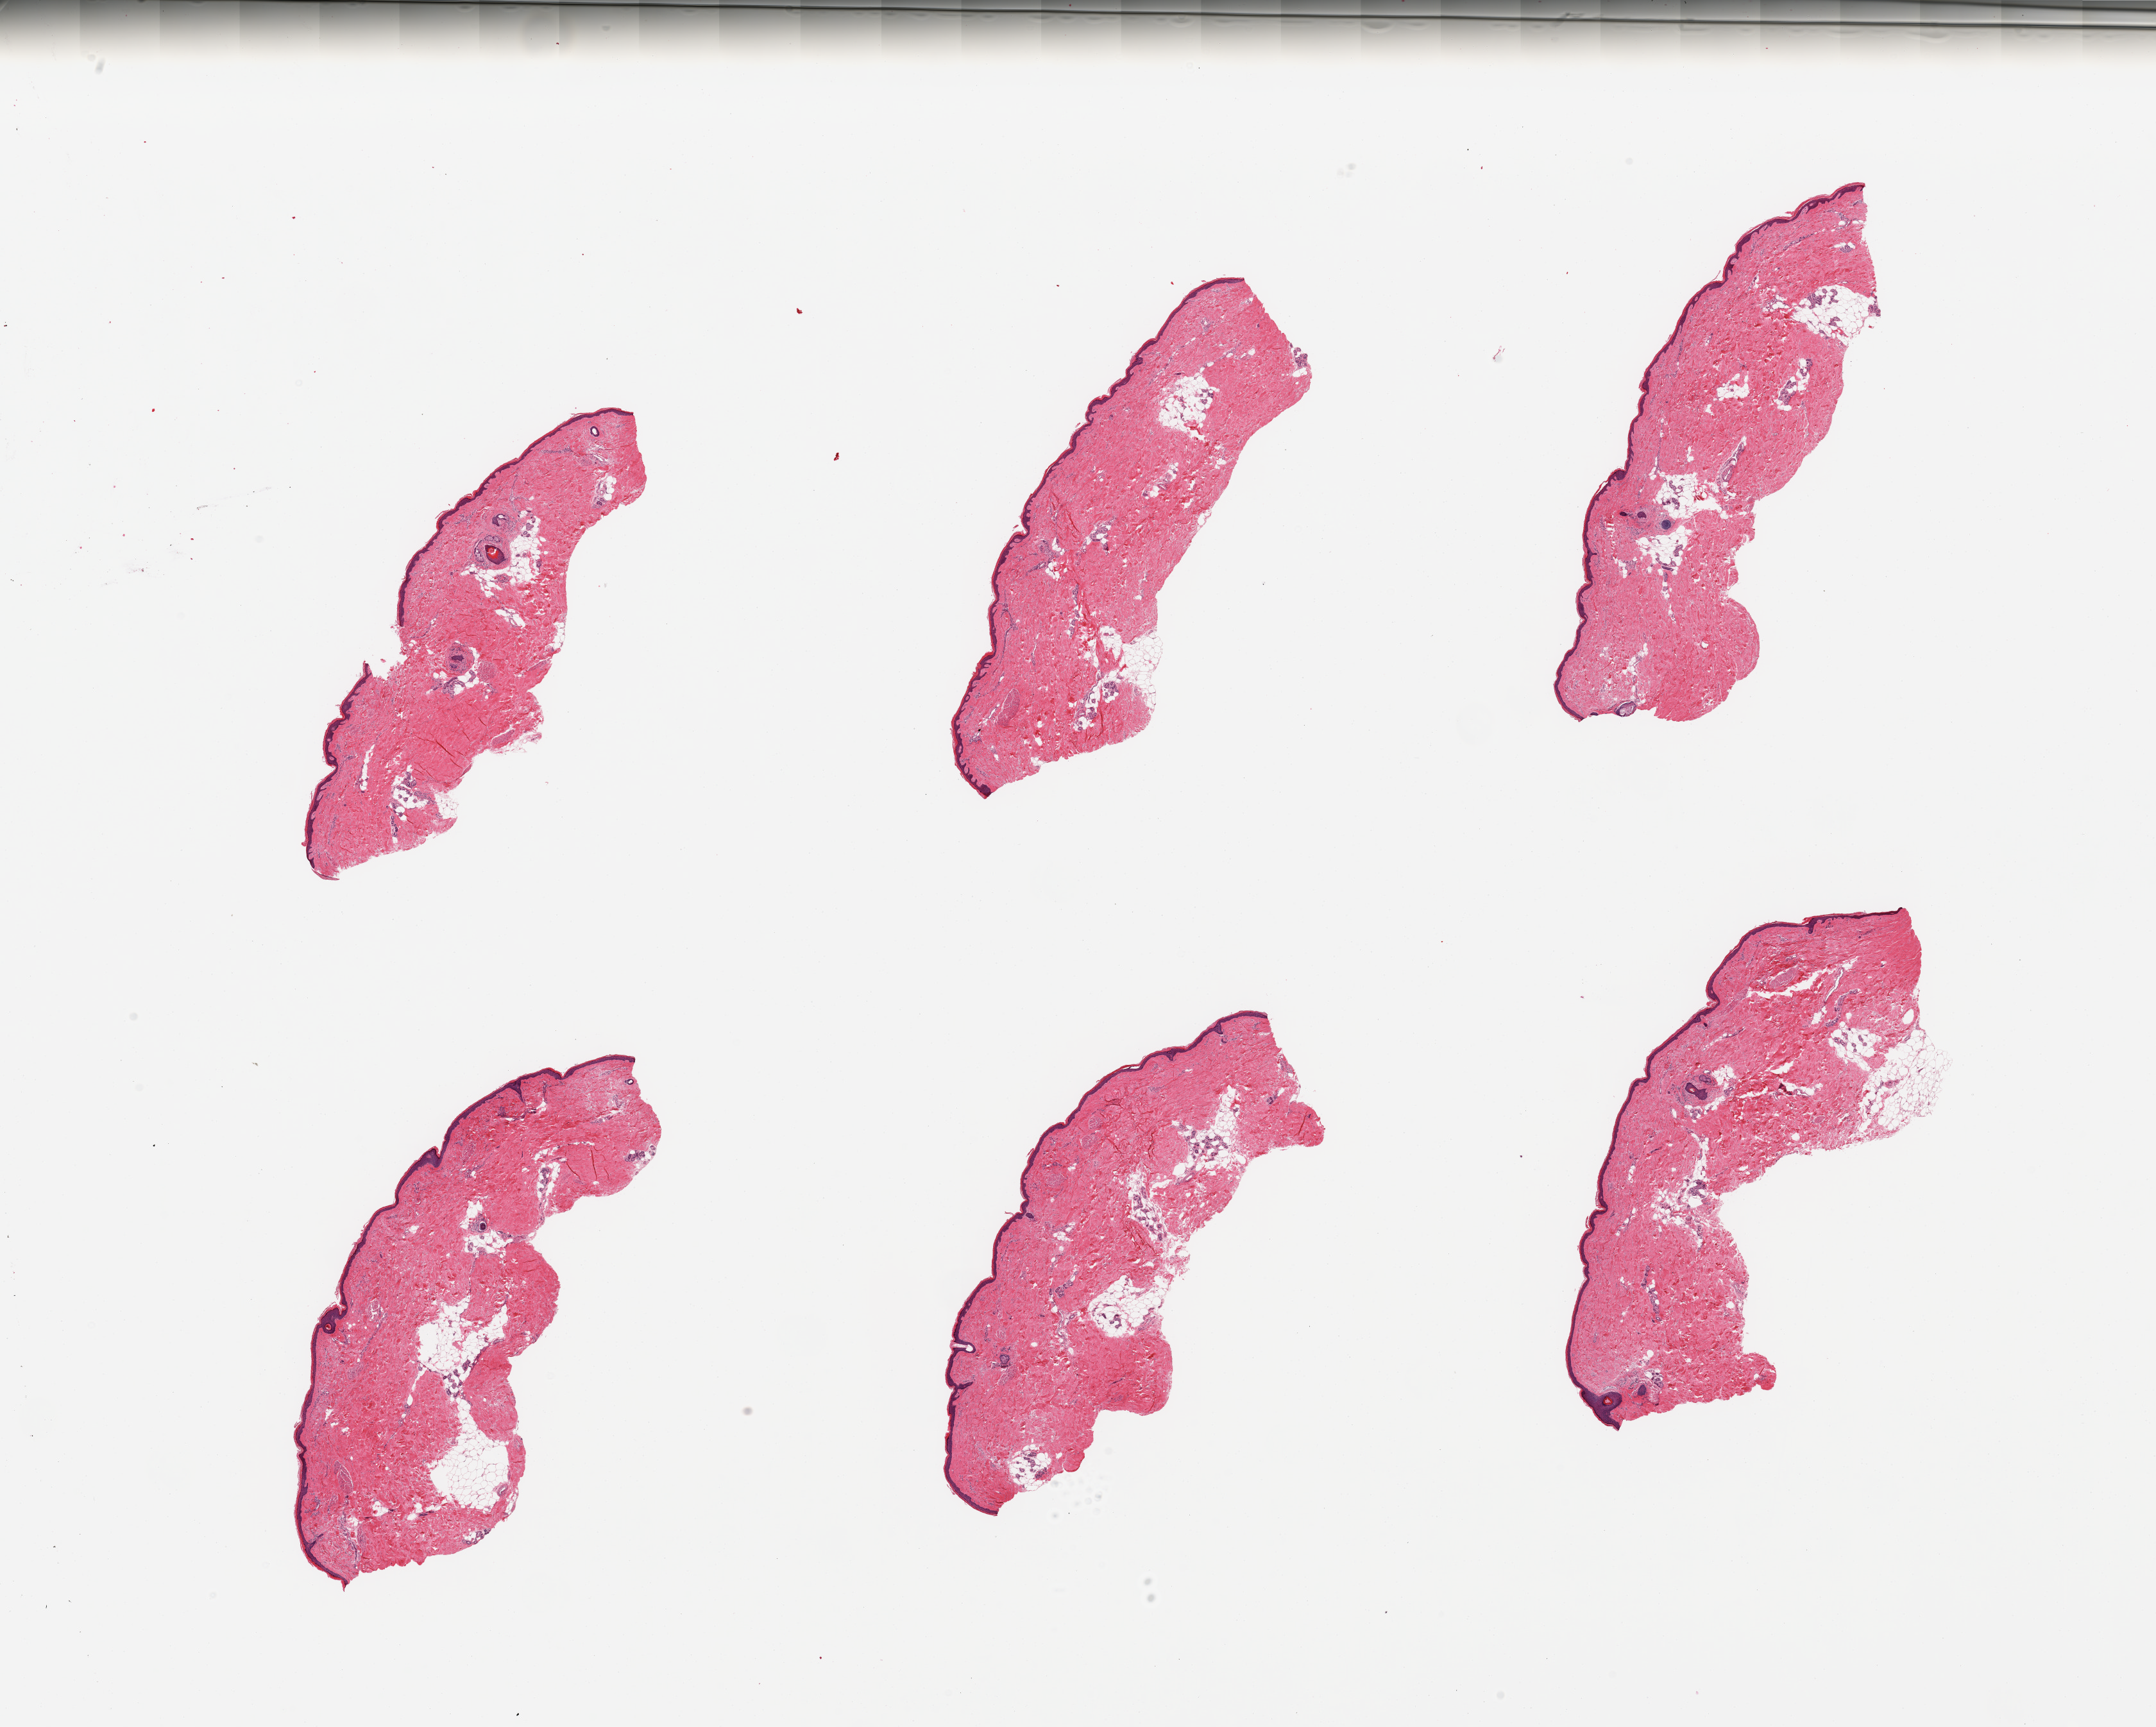
Whole-slide image, hematoxylin and eosin (H&E) stain — shown as a low-resolution overview of the whole scanned area (about 26.6 x 21.3 mm). PAXgene-fixed, paraffin-embedded tissue. Target tissue: skin of lower leg. Tissue donor sample. Donor: male.
Review note (as recorded): 6 pieces; well trimmed; 10% dermal fat.